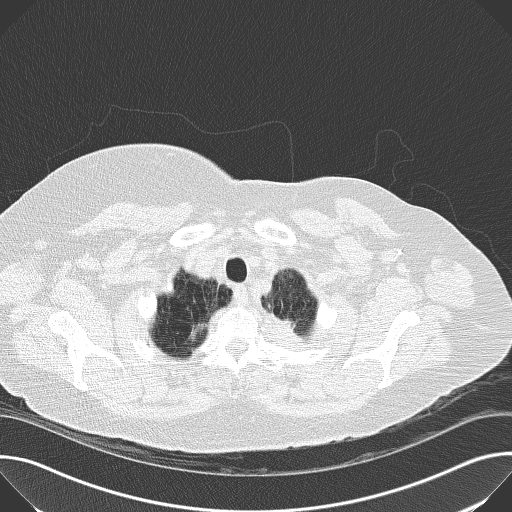
Low-dose screening chest CT, one axial slice; slice 154 of 169 in the series (ordered by position); reconstruction kernel B50f; 120 kVp; lung window (W 1500 / L -600 HU); 512 × 512 image matrix.
Annotated regions visible in this slice (expert manual segmentation):
- lesion 1 (tumor, upper lobe of left lung): bounding box (x1, y1, x2, y2) in pixels: (282, 319, 296, 331)